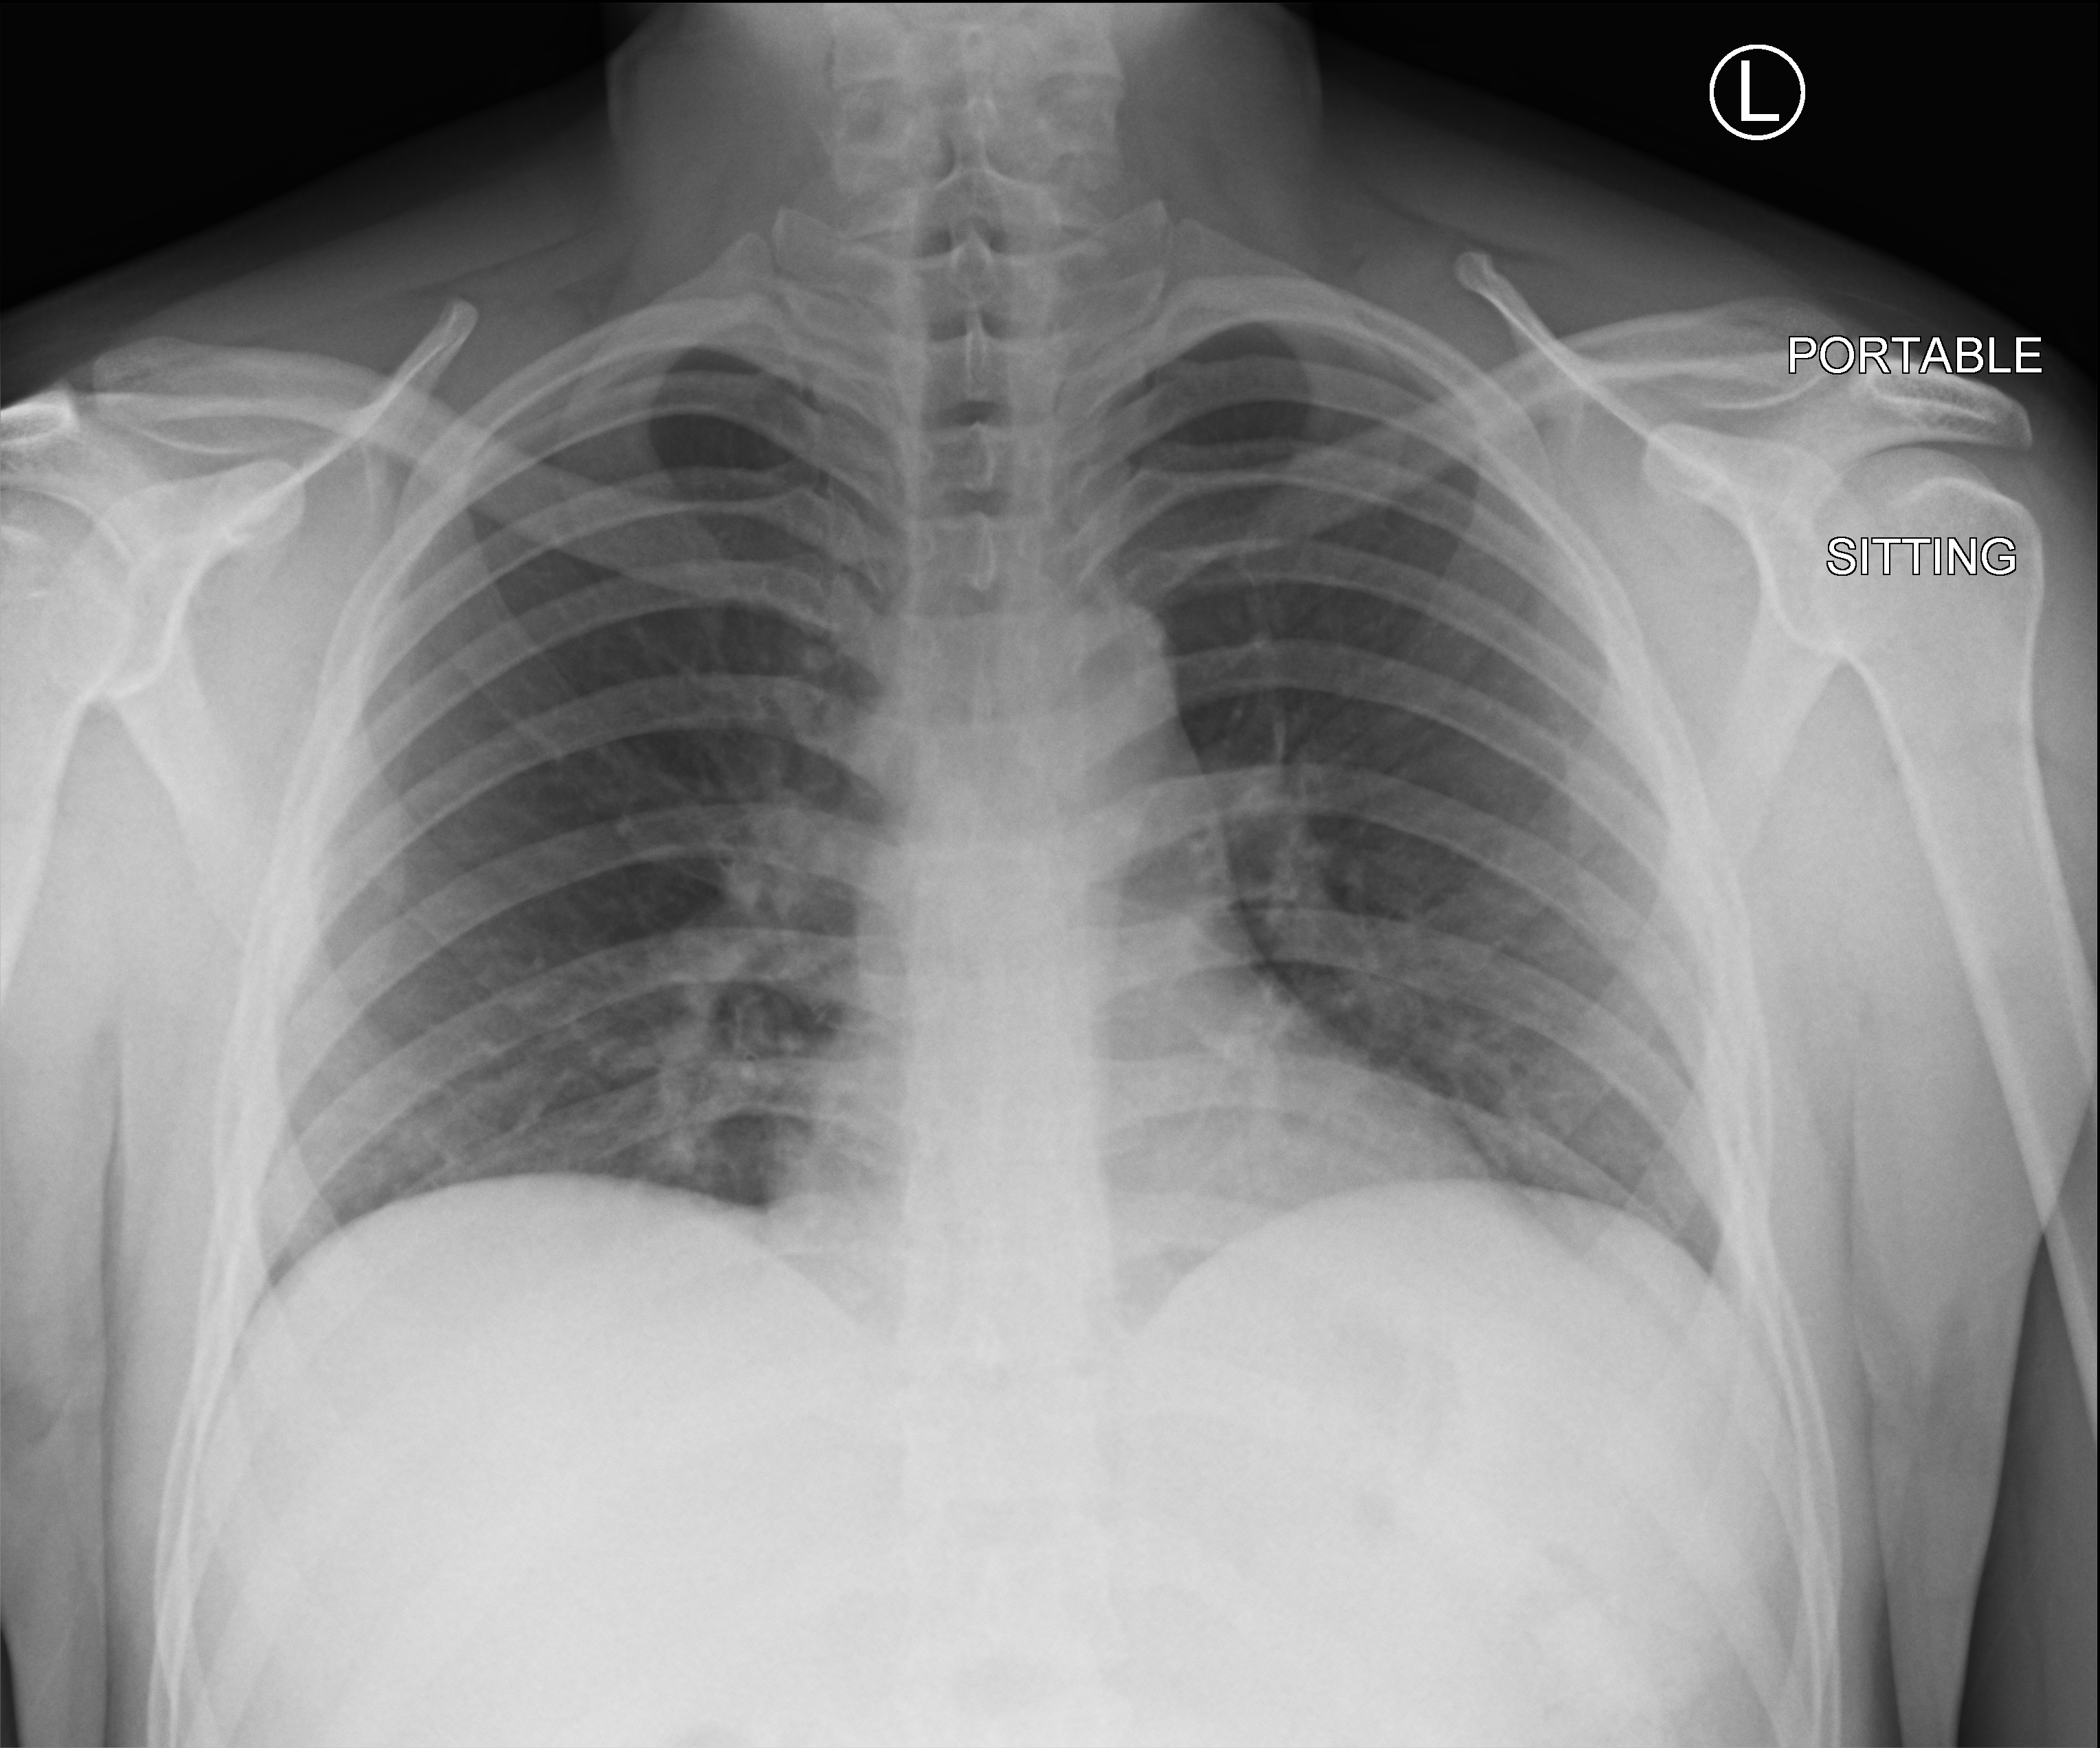
Portable chest radiograph, anteroposterior (AP) projection. Patient hospitalised with COVID-19; male, aged 18–59 years.
From the hospital-stay record, not from the radiograph (when in the stay this image was taken is not recorded): admitted to intensive care during this hospital stay: no; mechanically ventilated during this hospital stay: no.